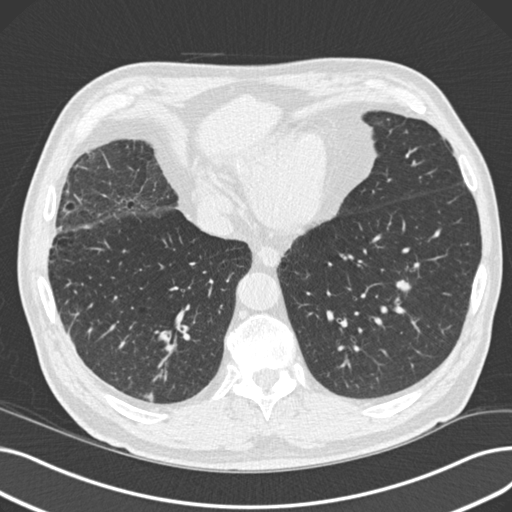
Low-dose screening chest CT, one axial slice. Position 41 of 165 along the scan axis. Reconstruction kernel B30f. 120 kVp. Lung window (W 1500 / L -600 HU). 2 mm slice thickness. 512 × 512 image matrix, field of view 369 × 369 mm.
Annotated regions visible in this slice (expert manual segmentation):
- lesion 1 (tumor, lower lobe of left lung): bounding box (x1, y1, x2, y2) in pixels: (396, 281, 410, 291)